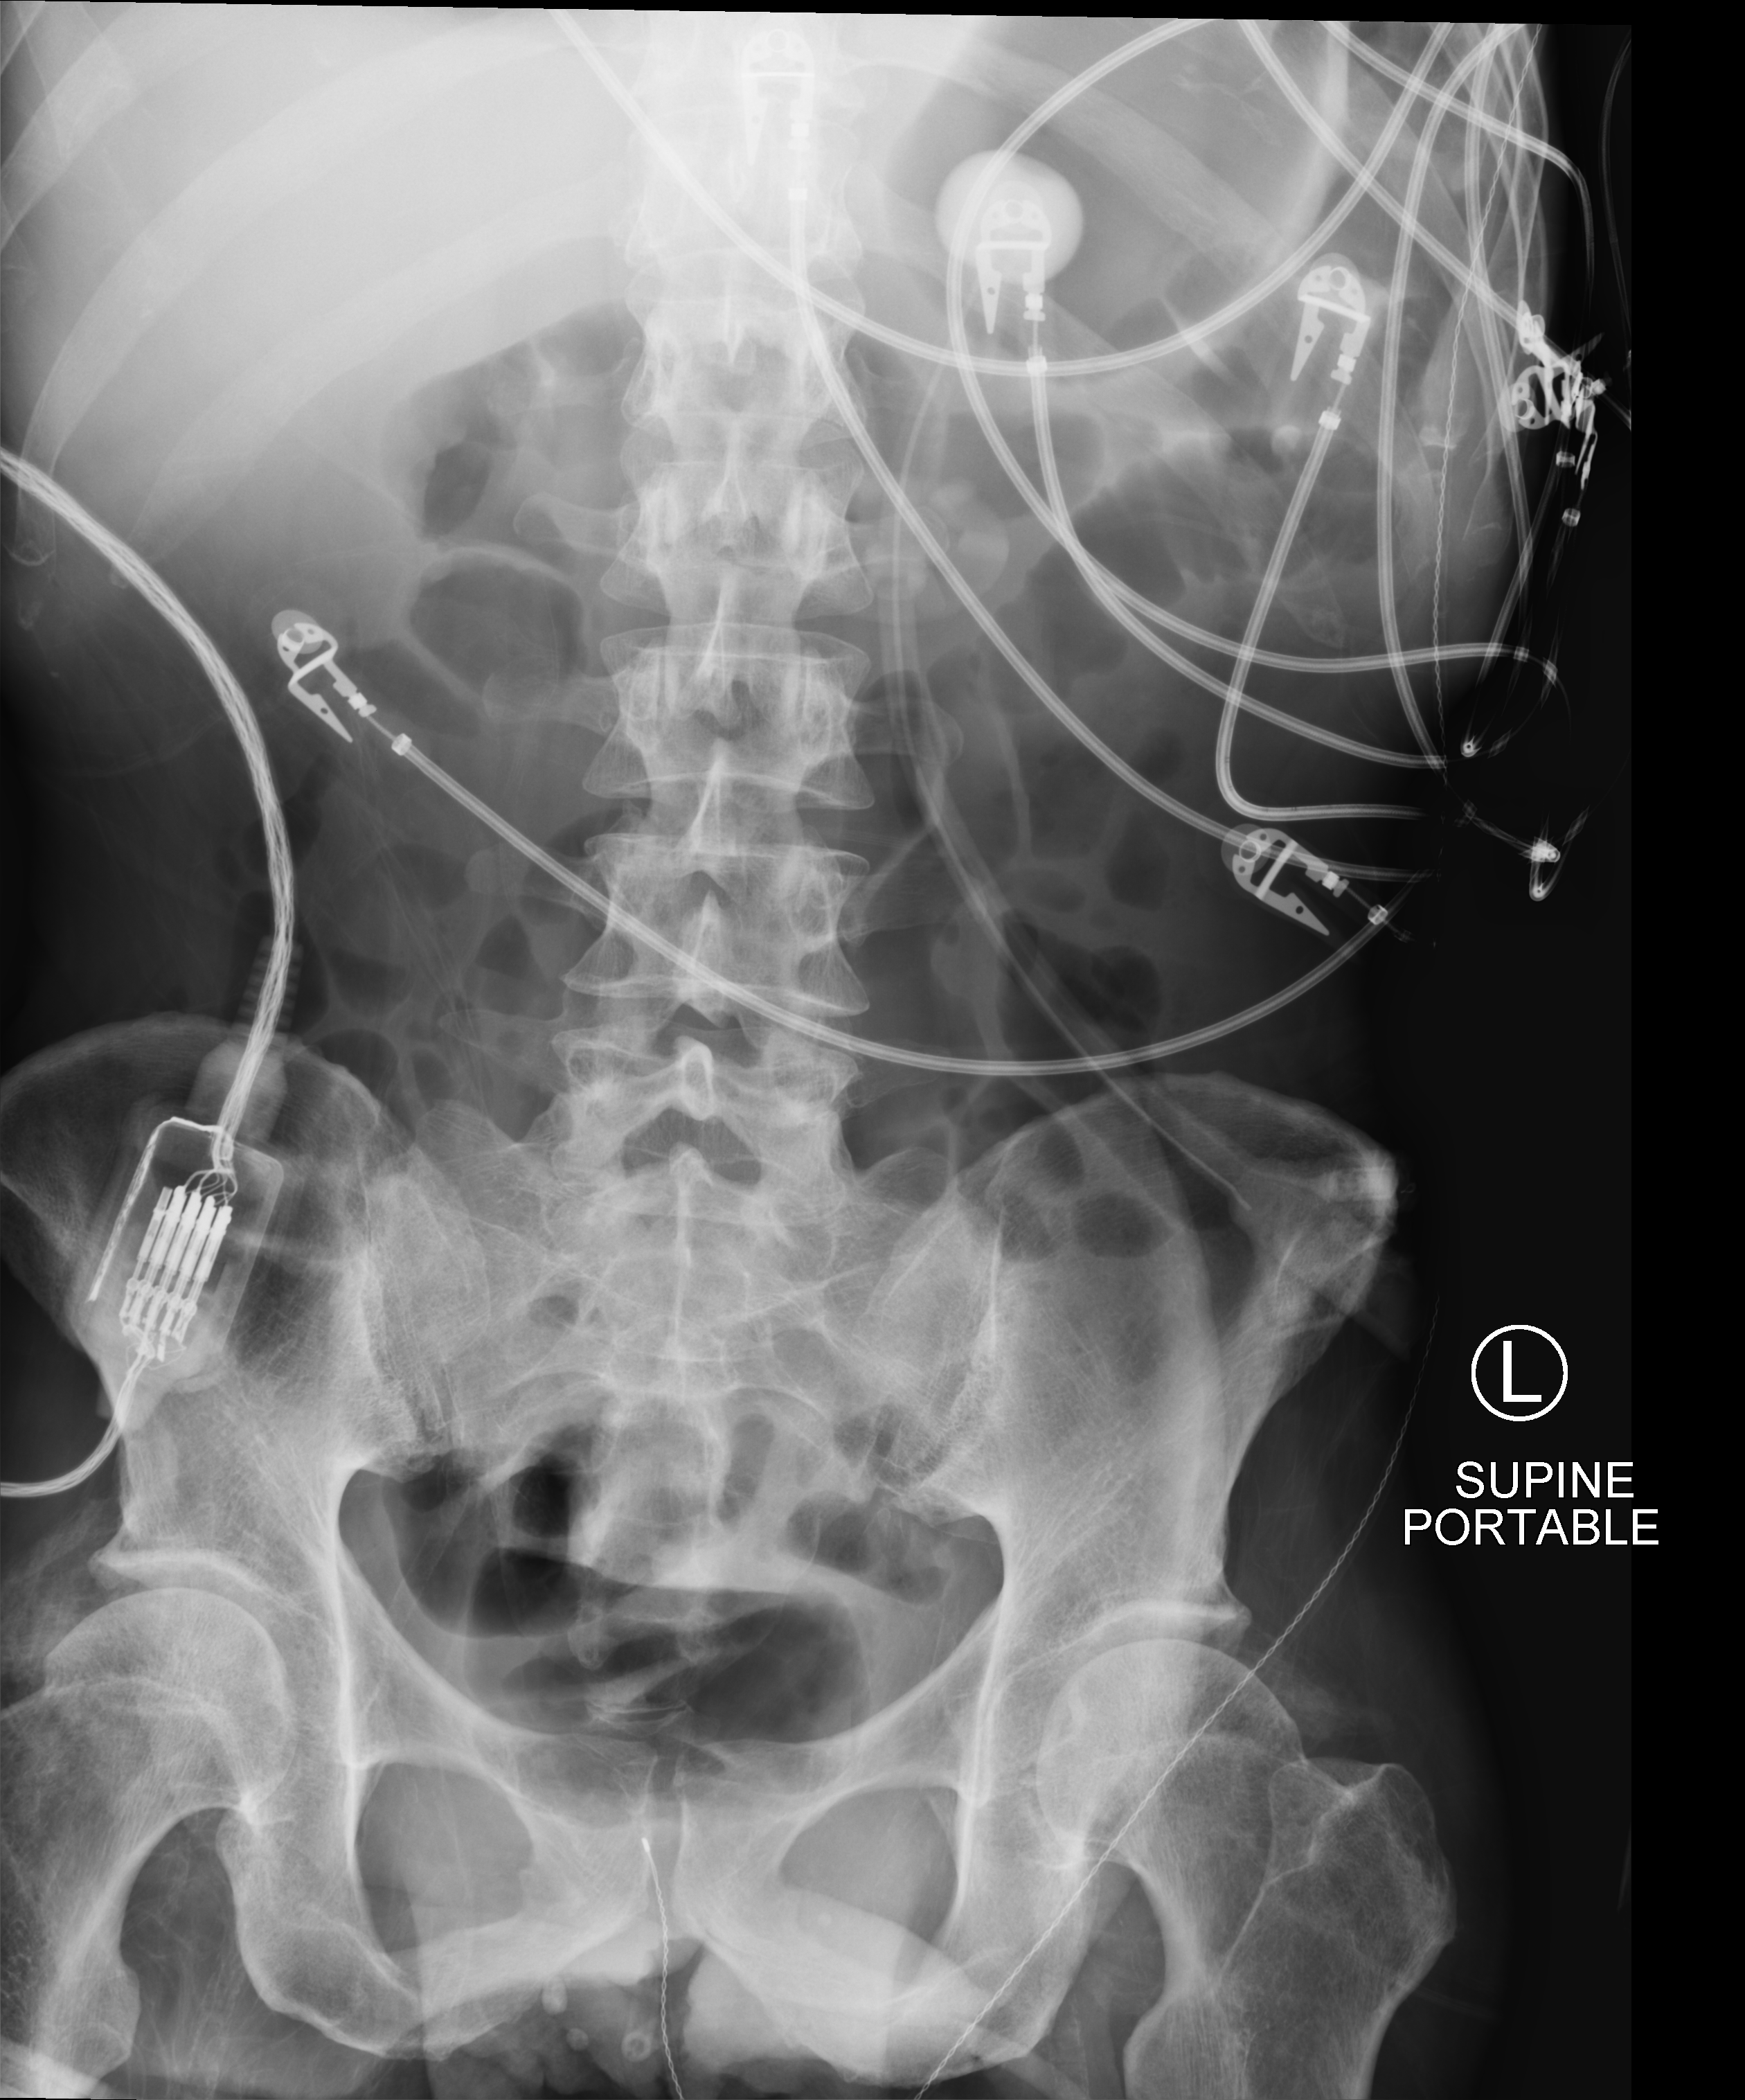
Portable abdomen radiograph, anteroposterior (AP) projection. Male patient hospitalised with COVID-19, age 18–59 years.
Hospital-stay facts (about this admission, not read from this image; timing relative to this image not recorded):
- smoking status (admission record): never